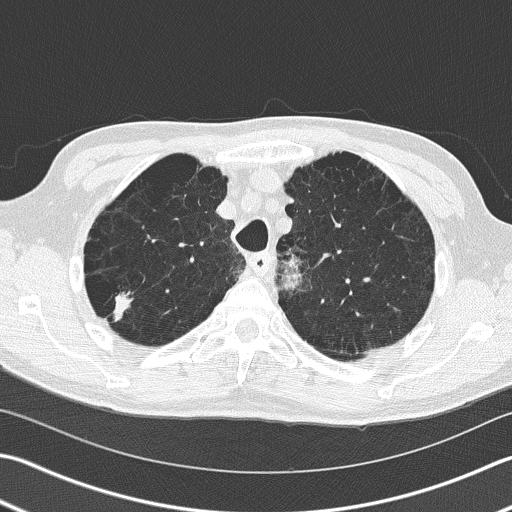
Low-dose screening chest CT, one axial slice. Position 125 of 163 along the scan axis. Reconstruction kernel B50f. 120 kVp. Lung window (W 1500 / L -600 HU). 2 mm slice thickness. 512 × 512 image matrix, field of view 346 × 346 mm.
Annotated regions visible in this slice (outlined manually by an expert reader):
- lesion 1 (tumor, upper lobe of right lung): bounding box [x1, y1, x2, y2] px = [114, 293, 131, 319]